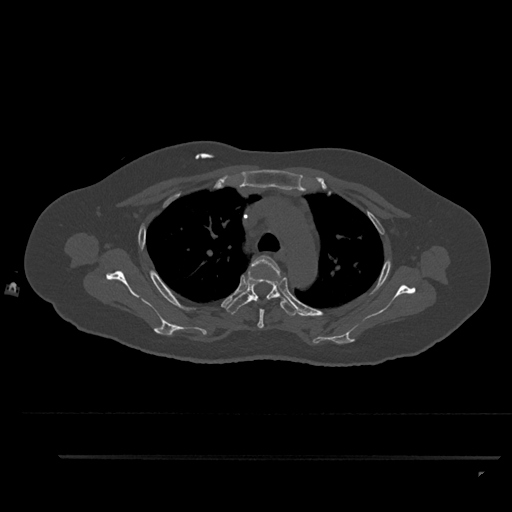
CT including the spine, one axial slice; bone window (W 1800 / L 400 HU); 512 × 512 image matrix, field of view 408 × 408 mm. Female patient, age 44 years. Case-level facts recorded for this patient, not image findings: primary cancer: renal; vertebrae with lytic lesions (as recorded): L1.
Annotated regions visible in this slice (semi-automatic segmentation, software-assisted and operator-edited):
- T3 vertebra: bounding box <250,255,282,328> (left, top, right, bottom; pixels)
- T4 vertebra: <226,270,298,316>